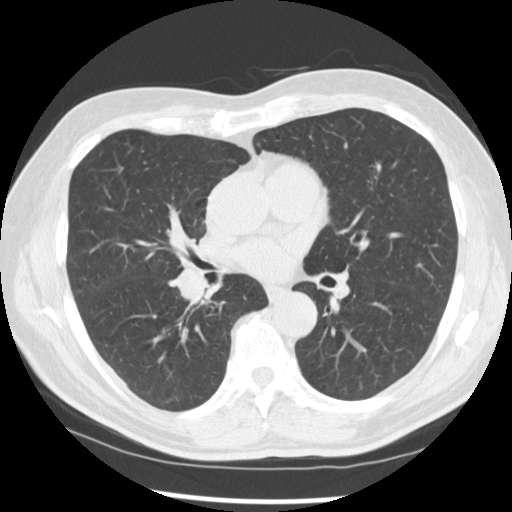
Low-dose screening chest CT, one axial slice; position 147 of 277 along the scan axis; reconstruction kernel STANDARD; 120 kVp; lung window (W 1500 / L -600 HU); 2.5 mm slice thickness; 512 × 512 image matrix, field of view 365 × 365 mm.
Structures marked on this image (manually delineated by an expert):
- lesion 1 (tumor, middle lobe of right lung): bounding box [x1, y1, x2, y2] px = [175, 264, 209, 301]